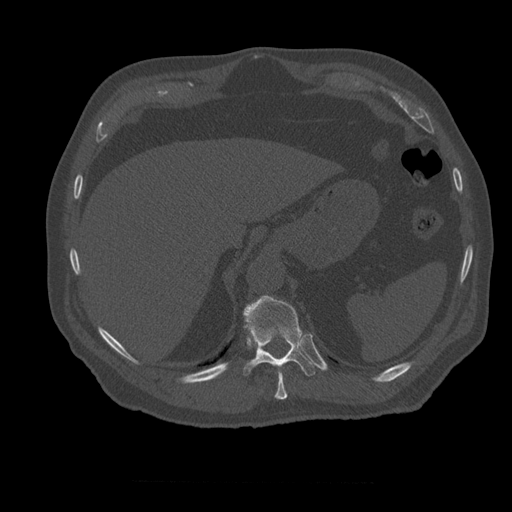
CT including the spine, one axial slice. Position 284 of 399 along the scan axis. Reconstruction kernel STANDARD. 120 kVp. Bone window (W 1800 / L 400 HU). 512 × 512 image matrix. Patient age 73 years. Case-level facts recorded for this patient, not image findings: primary cancer: prostate; vertebrae with lytic lesions (as recorded): L2.
Structures marked on this image (semi-automatically segmented with operator editing):
- T10 vertebra: bounding box <275,371,288,400> (left, top, right, bottom; pixels)
- T11 vertebra: <243,295,315,376>